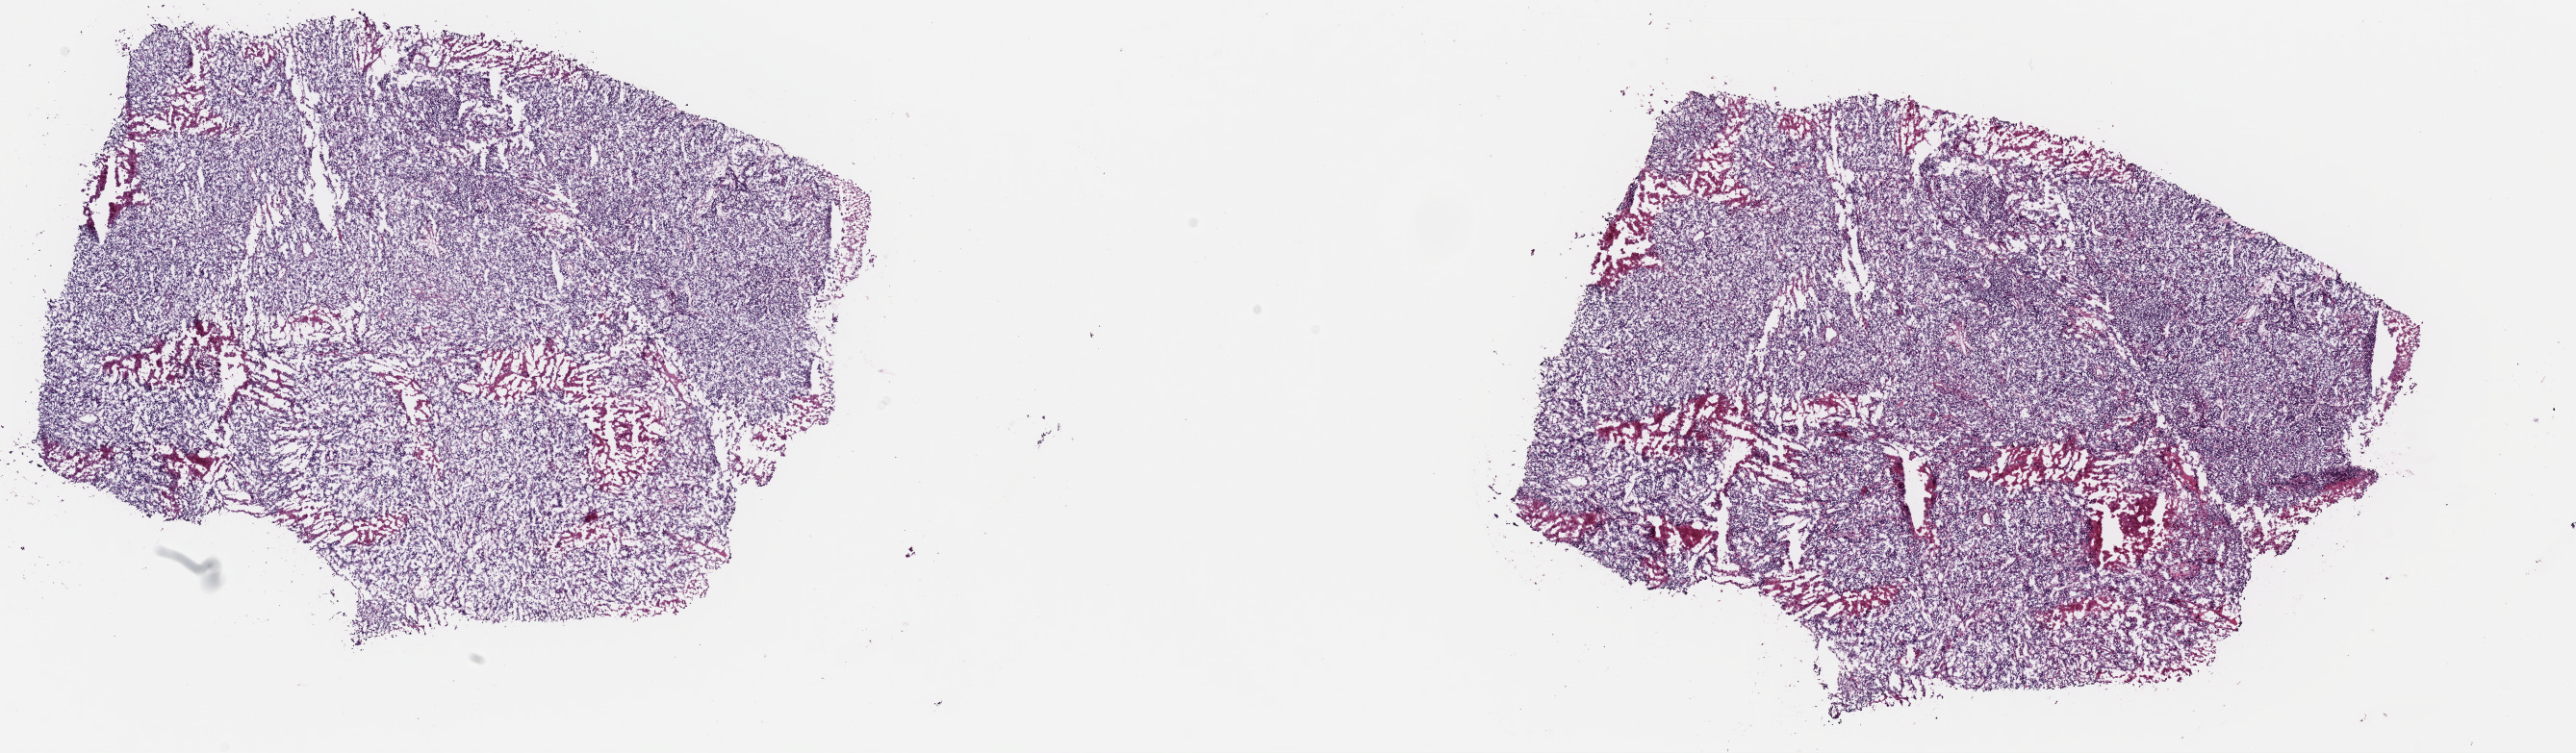
H&E-stained whole-slide image, a low-resolution overview of the entire scanned area, about 21.1 x 6.2 mm (slide scanned at 40x); frozen section from the top of the tissue portion; uterus, primary tumour sample. Patient: female, age at initial diagnosis 79 years. Histologic grade: G3 (poorly differentiated). Slide review estimates, as recorded: tumour cells 90%, tumour nuclei 90%, normal cells 0%, stromal cells 5%, necrosis 5%. Inflammatory infiltration, as recorded: lymphocyte infiltration 40%, monocyte infiltration 20%, neutrophil infiltration 20%.
* FIGO stage: IA
* histologic diagnosis: Endometrioid adenocarcinoma, NOS (endometrium)